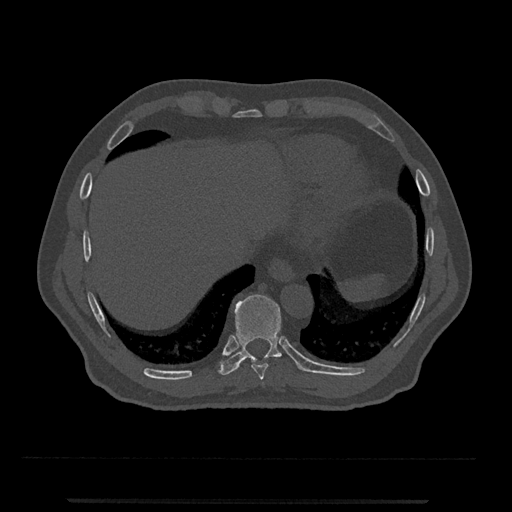
CT including the spine, one axial slice; position 541 of 797 along the scan axis; reconstruction kernel Br40s/3; 120 kVp; bone window (W 1800 / L 400 HU); 512 × 512 image matrix, field of view 419 × 419 mm. Patient: male, 63 years. From the clinical record (not read from this slice): primary cancer: prostate.
Structures marked on this image (semi-automatically segmented with operator editing):
- T10 vertebra: box from (x=218, y=294) to (x=282, y=375) px
- T9 vertebra: (x=251, y=363)–(x=268, y=380)